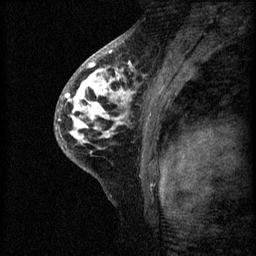
Breast MRI (dynamic contrast-enhanced), one sagittal slice. Slice 40 of 60 in the series (ordered by position). 3 images stored at this slice position (order not interpretable as contrast timing). 1.5 T. TE 4.2 ms, TR 8.2 ms. 2 mm slice thickness. 256 × 256 image matrix, field of view 180 × 180 mm. Patient: female, 41 years.
Annotated regions visible in this slice (semi-automatic segmentation, software-assisted and operator-edited):
- analysis volume of interest (the breast-tissue region the enhancement analysis was run in; not a lesion): bounding box <55,62,160,175> (left, top, right, bottom; pixels)
- tumour enhancement mask (voxels above the 70 % enhancement threshold inside the analysis volume of interest): <58,62,136,153>